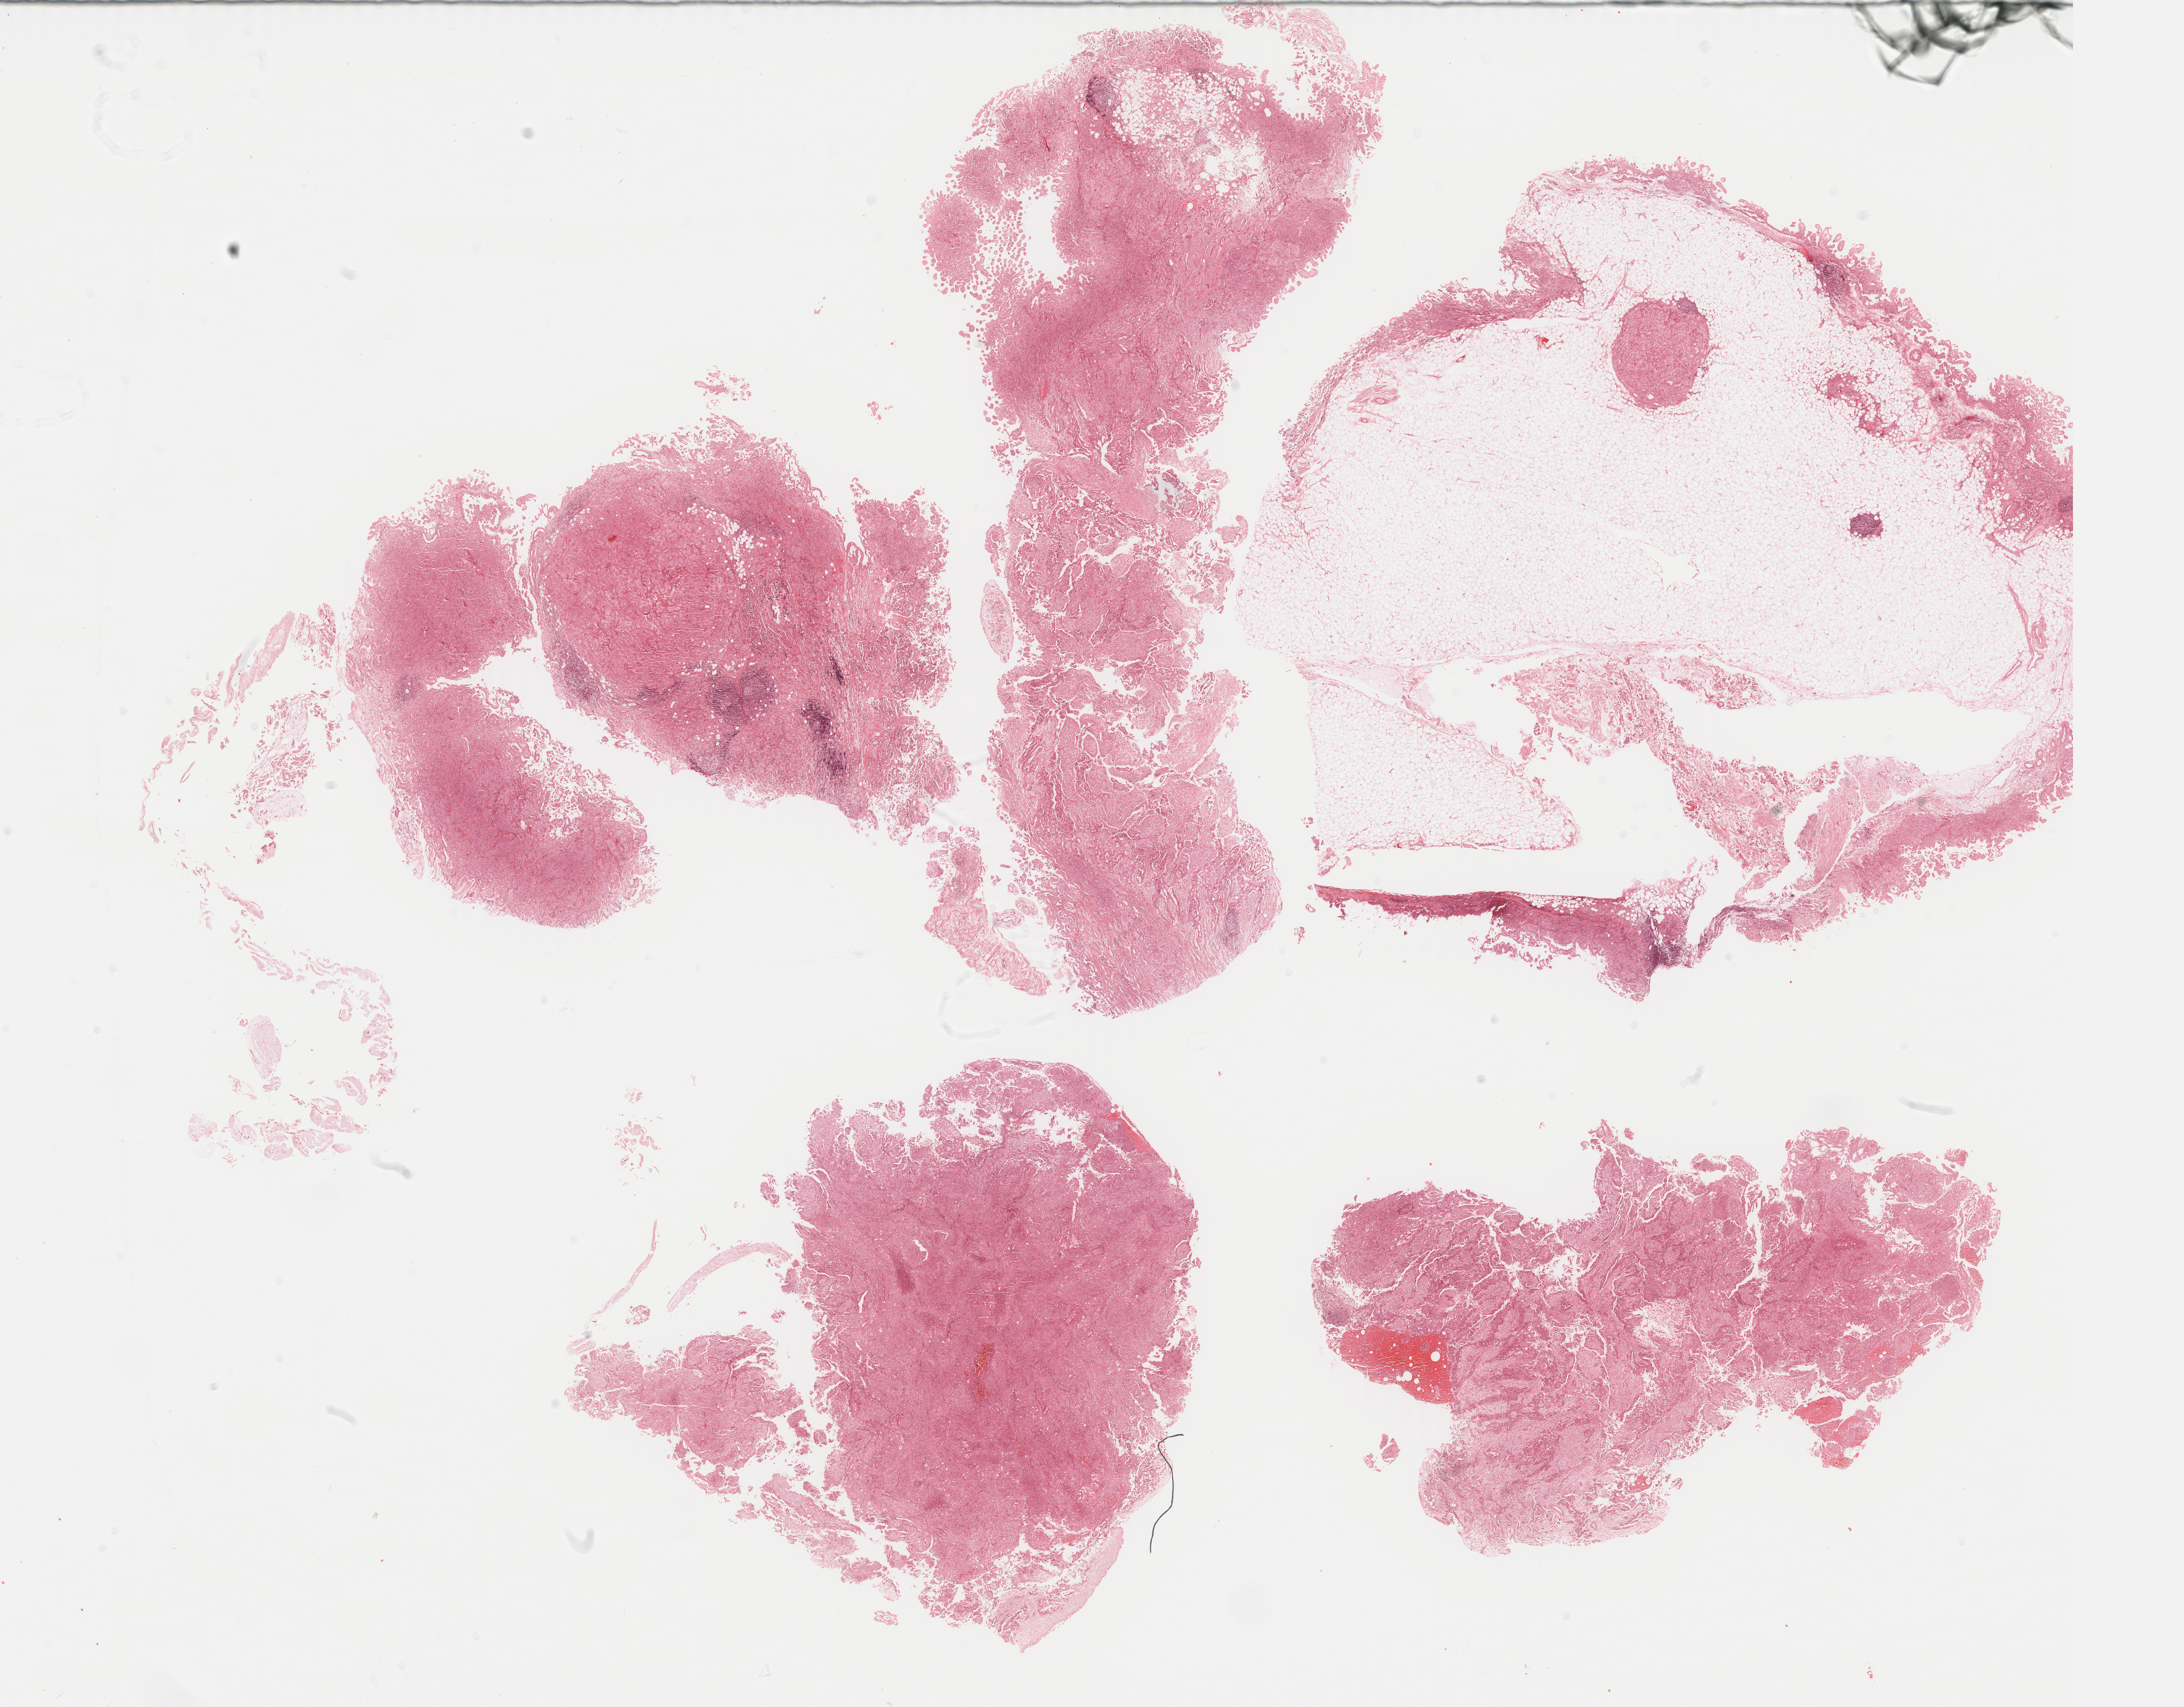
Digitized H&E tissue section (whole slide), whole scanned area (about 28.0 x 21.9 mm, from a 40x scan) shown as a low-resolution overview. Formalin-fixed paraffin-embedded (FFPE) diagnostic section. Primary tumour sample from the mesothelium. Patient: male, age at initial diagnosis 65 years.
• TNM: T2 N2 M0
• diagnosis: Mesothelioma, malignant (pleura, NOS)
• AJCC pathologic stage: III